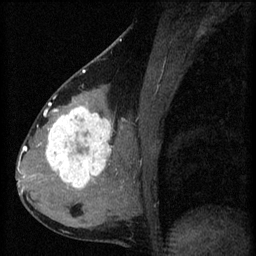
Breast MRI (dynamic contrast-enhanced), one sagittal slice. Position 29 of 60 along the scan axis. 3 images stored at this slice position (order not interpretable as contrast timing). 1.5 T. TE 4.2 ms, TR 8.2 ms. 2 mm slice thickness. 256 × 256 image matrix, field of view 180 × 180 mm. Female patient, age 37 years.
Annotated regions visible in this slice (semi-automatically segmented with operator editing):
- analysis volume of interest (the breast-tissue region the enhancement analysis was run in; not a lesion): bounding box <44,100,119,197> (left, top, right, bottom; pixels)
- tumour enhancement mask (voxels above the 70 % enhancement threshold inside the analysis volume of interest): <47,106,113,189>